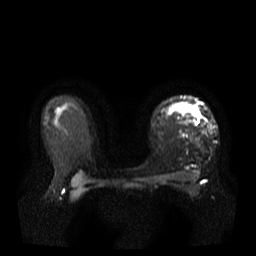
Breast MRI, one axial slice; slice 26 of 37 in the series (ordered by position); diffusion-weighted series; image 2 of 4 stored at this slice position (different b-values; order by instance number); 3 T; 5 mm slice thickness; 256 × 256 image matrix. Female patient.
Structures marked on this image (expert manual segmentation):
- tumour on diffusion-weighted imaging: bounding box [x1, y1, x2, y2] px = [197, 116, 199, 118]